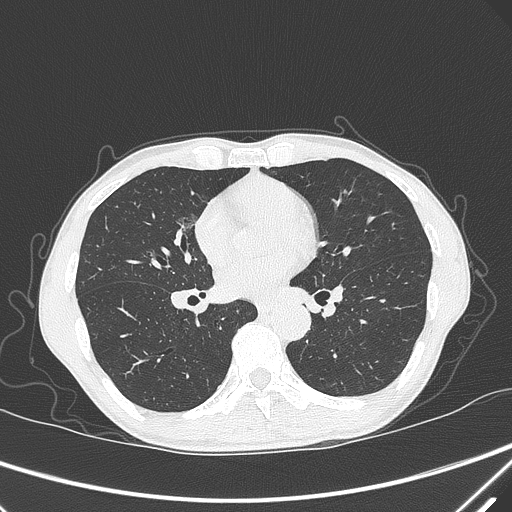
Chest CT, one axial slice; slice 161 of 339 in the series (ordered by position); 120 kVp; lung window (W 1500 / L -600 HU); 1 mm slice thickness; 512 × 512 image matrix. Male patient, age 67 years. From the clinical record (not read from this slice): clinical TNM (as recorded): T1c N0 M0.
Structures marked on this image (bounding box drawn by a radiologist):
- lung tumour (recorded histology: adenocarcinoma): bounding box [x1, y1, x2, y2] px = [171, 209, 198, 235]